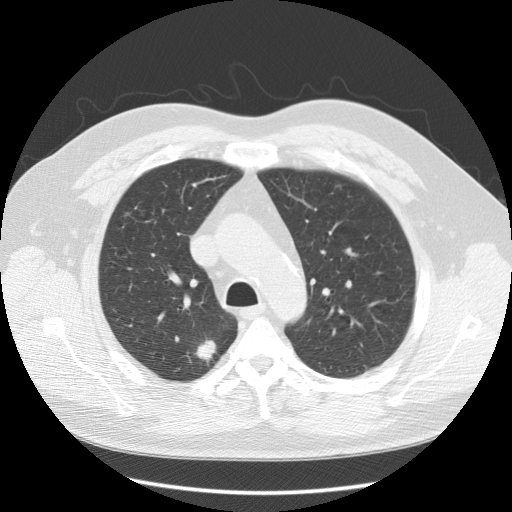
Chest CT (low-dose screening protocol), one axial image, baseline screening round, lung window (W 1500 / L -600 HU), 2.5 mm slice thickness, standard (soft-tissue) reconstruction kernel (STANDARD). Male, age 55 years at enrolment.
Expert reader's lesion annotation, bounding box [x1, y1, x2, y2] px = [184, 329, 232, 376]. The screening reader recorded 2 non-calcified nodules or masses ≥4 mm on this exam (right upper lobe, left upper lobe); which of them this box marks is not recorded. Official screen result: positive, change unspecified: nodule(s) >= 4 mm or enlarging nodule(s), mass(es), or other non-specific abnormalities suspicious for lung cancer. Later outcome: lung cancer diagnosed 84 days after this screen — large cell neuroendocrine carcinoma, right upper lobe, poorly differentiated (G3), stage IA (AJCC 6th edition), 18 mm at pathology.